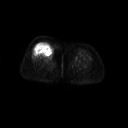
FDG PET of an extremity soft-tissue mass (from a PET/CT study), one axial slice. Position 31 of 267 along the scan axis. 3.27 mm slice thickness. 128 × 128 image matrix. Patient: female, 56 years. From the clinical record (not read from this slice): histological type: malignant solitary fibrous tumor; grade: intermediate; site of the primary tumour: right thigh.
Structures marked on this image (expert contour drawn on MRI and transferred to this co-registered scan by the dataset authors):
- gross tumour volume including surrounding oedema: bounding box [x1, y1, x2, y2] px = [35, 41, 55, 58]
- gross tumour volume (mass): [36, 41, 54, 57]